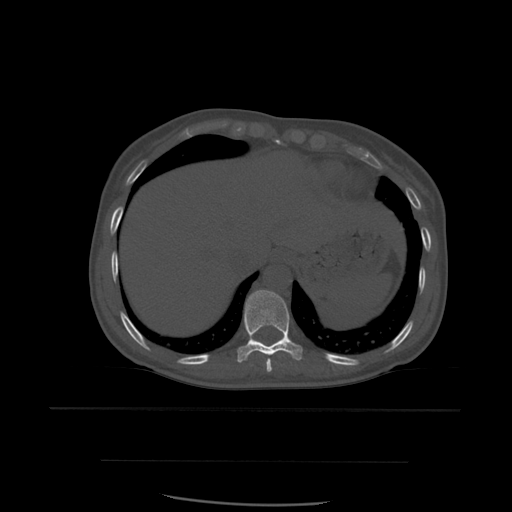
CT including the spine, one axial slice. Position 317 of 574 along the scan axis. Bone window (W 1800 / L 400 HU). 512 × 512 image matrix, field of view 392 × 392 mm. Patient age 48 years. Case-level facts recorded for this patient, not image findings: primary cancer: lung; vertebrae with lytic lesions (as recorded): T11.
Annotated regions visible in this slice (semi-automatic segmentation, software-assisted and operator-edited):
- T10 vertebra: bounding box <237,290,303,363> (left, top, right, bottom; pixels)
- T11 vertebra: <263,344,265,346>
- T9 vertebra: <267,359,273,372>